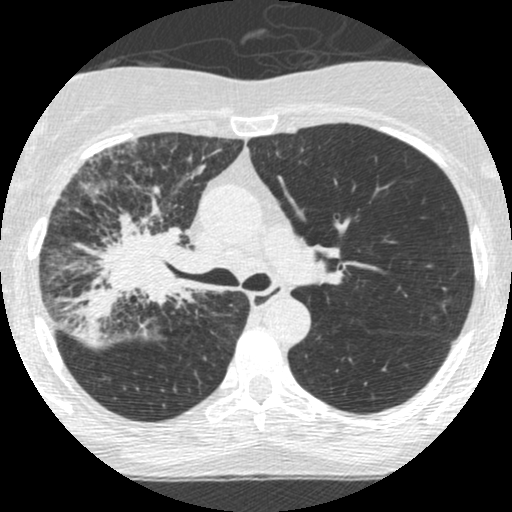
Low-dose screening chest CT, one axial slice; slice 168 of 253 in the series (ordered by position); reconstruction kernel STANDARD; 120 kVp; lung window (W 1500 / L -600 HU); 1.25 mm slice thickness; 512 × 512 image matrix, field of view 294 × 294 mm.
Structures marked on this image (expert manual segmentation):
- lesion 2 (tumor, hilum of right lung): bounding box <73,197,190,326> (left, top, right, bottom; pixels)